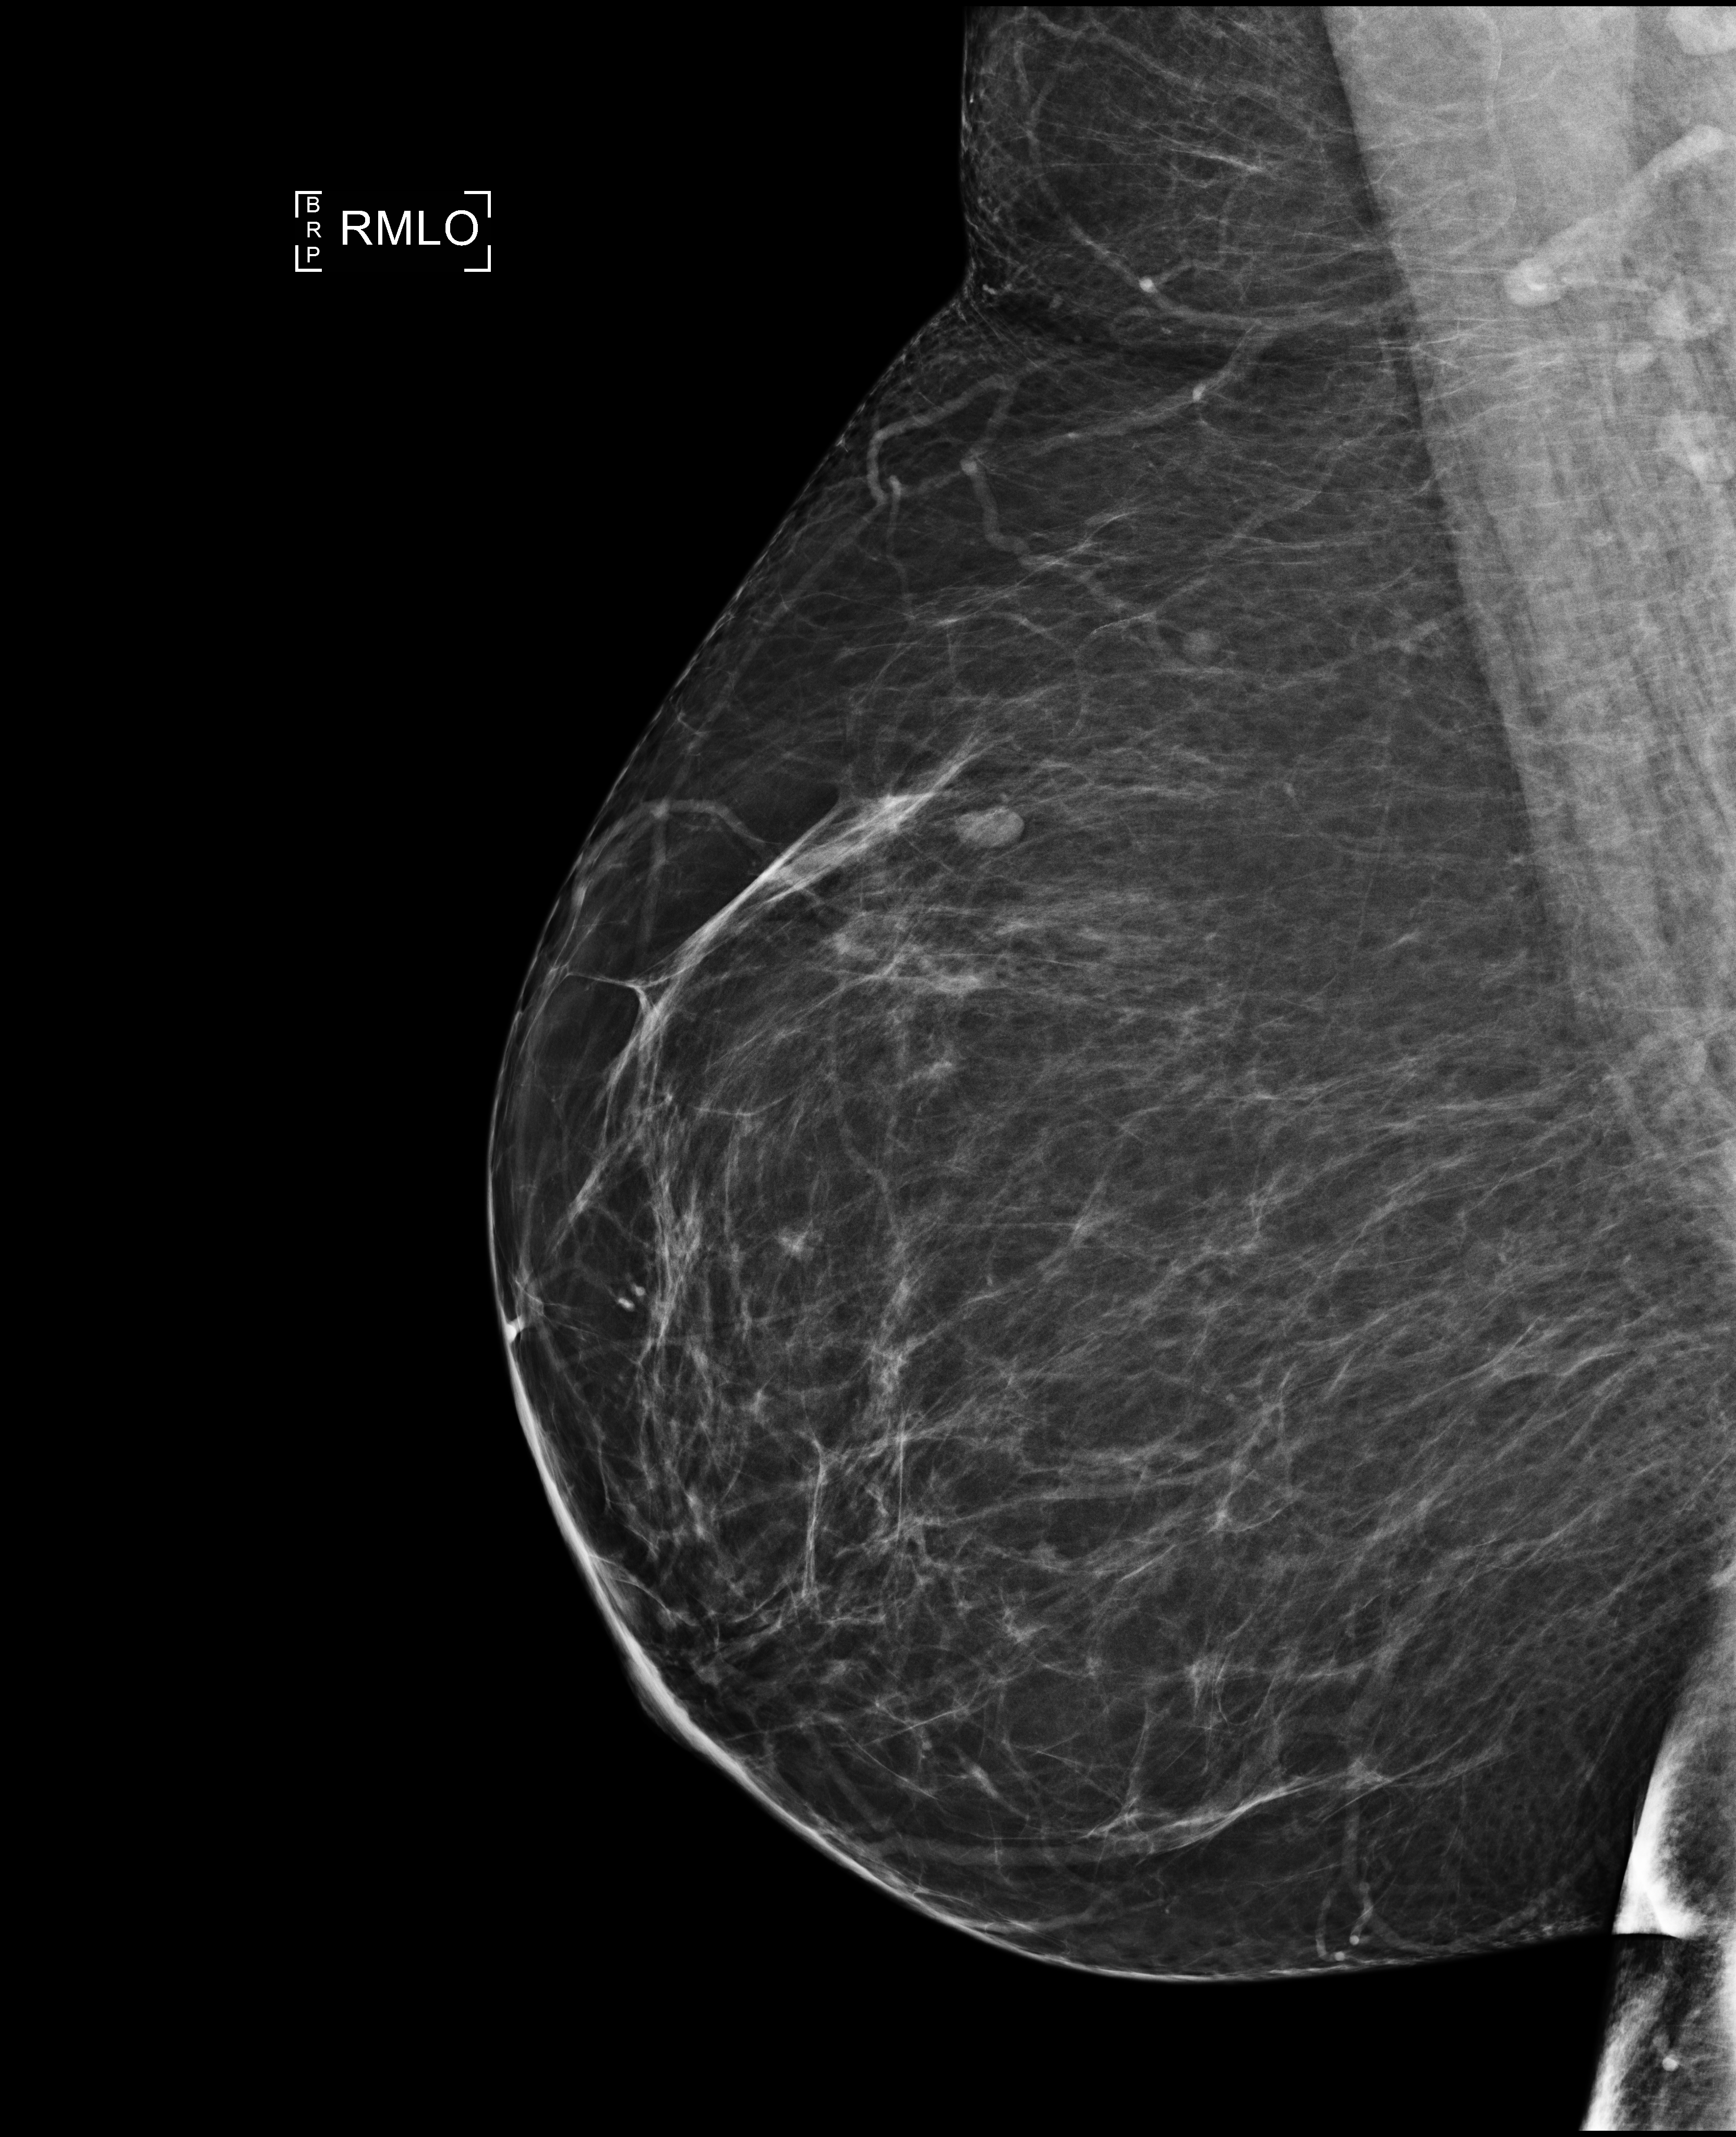
Screening examination. Patient: female, 51 years.
Image type: full-field digital mammogram. Breast: right. Projection: medio-lateral oblique projection.